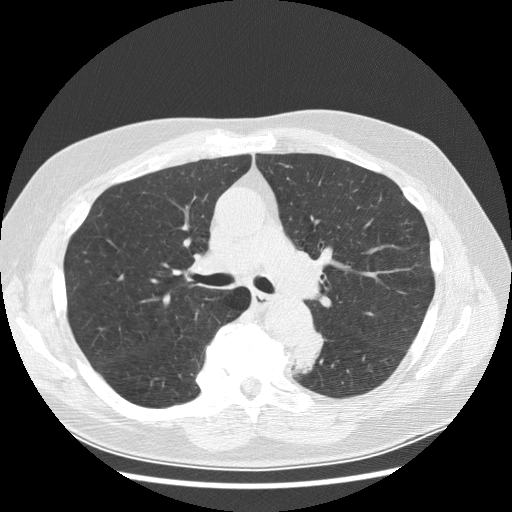
Low-dose screening chest CT, one axial slice. Slice 180 of 282 in the series (ordered by position). Lung window (W 1500 / L -600 HU). 512 × 512 image matrix, field of view 370 × 370 mm.
Structures marked on this image (expert manual segmentation):
- lesion 1 (tumor, lower lobe of left lung): bounding box <293,330,325,374> (left, top, right, bottom; pixels)